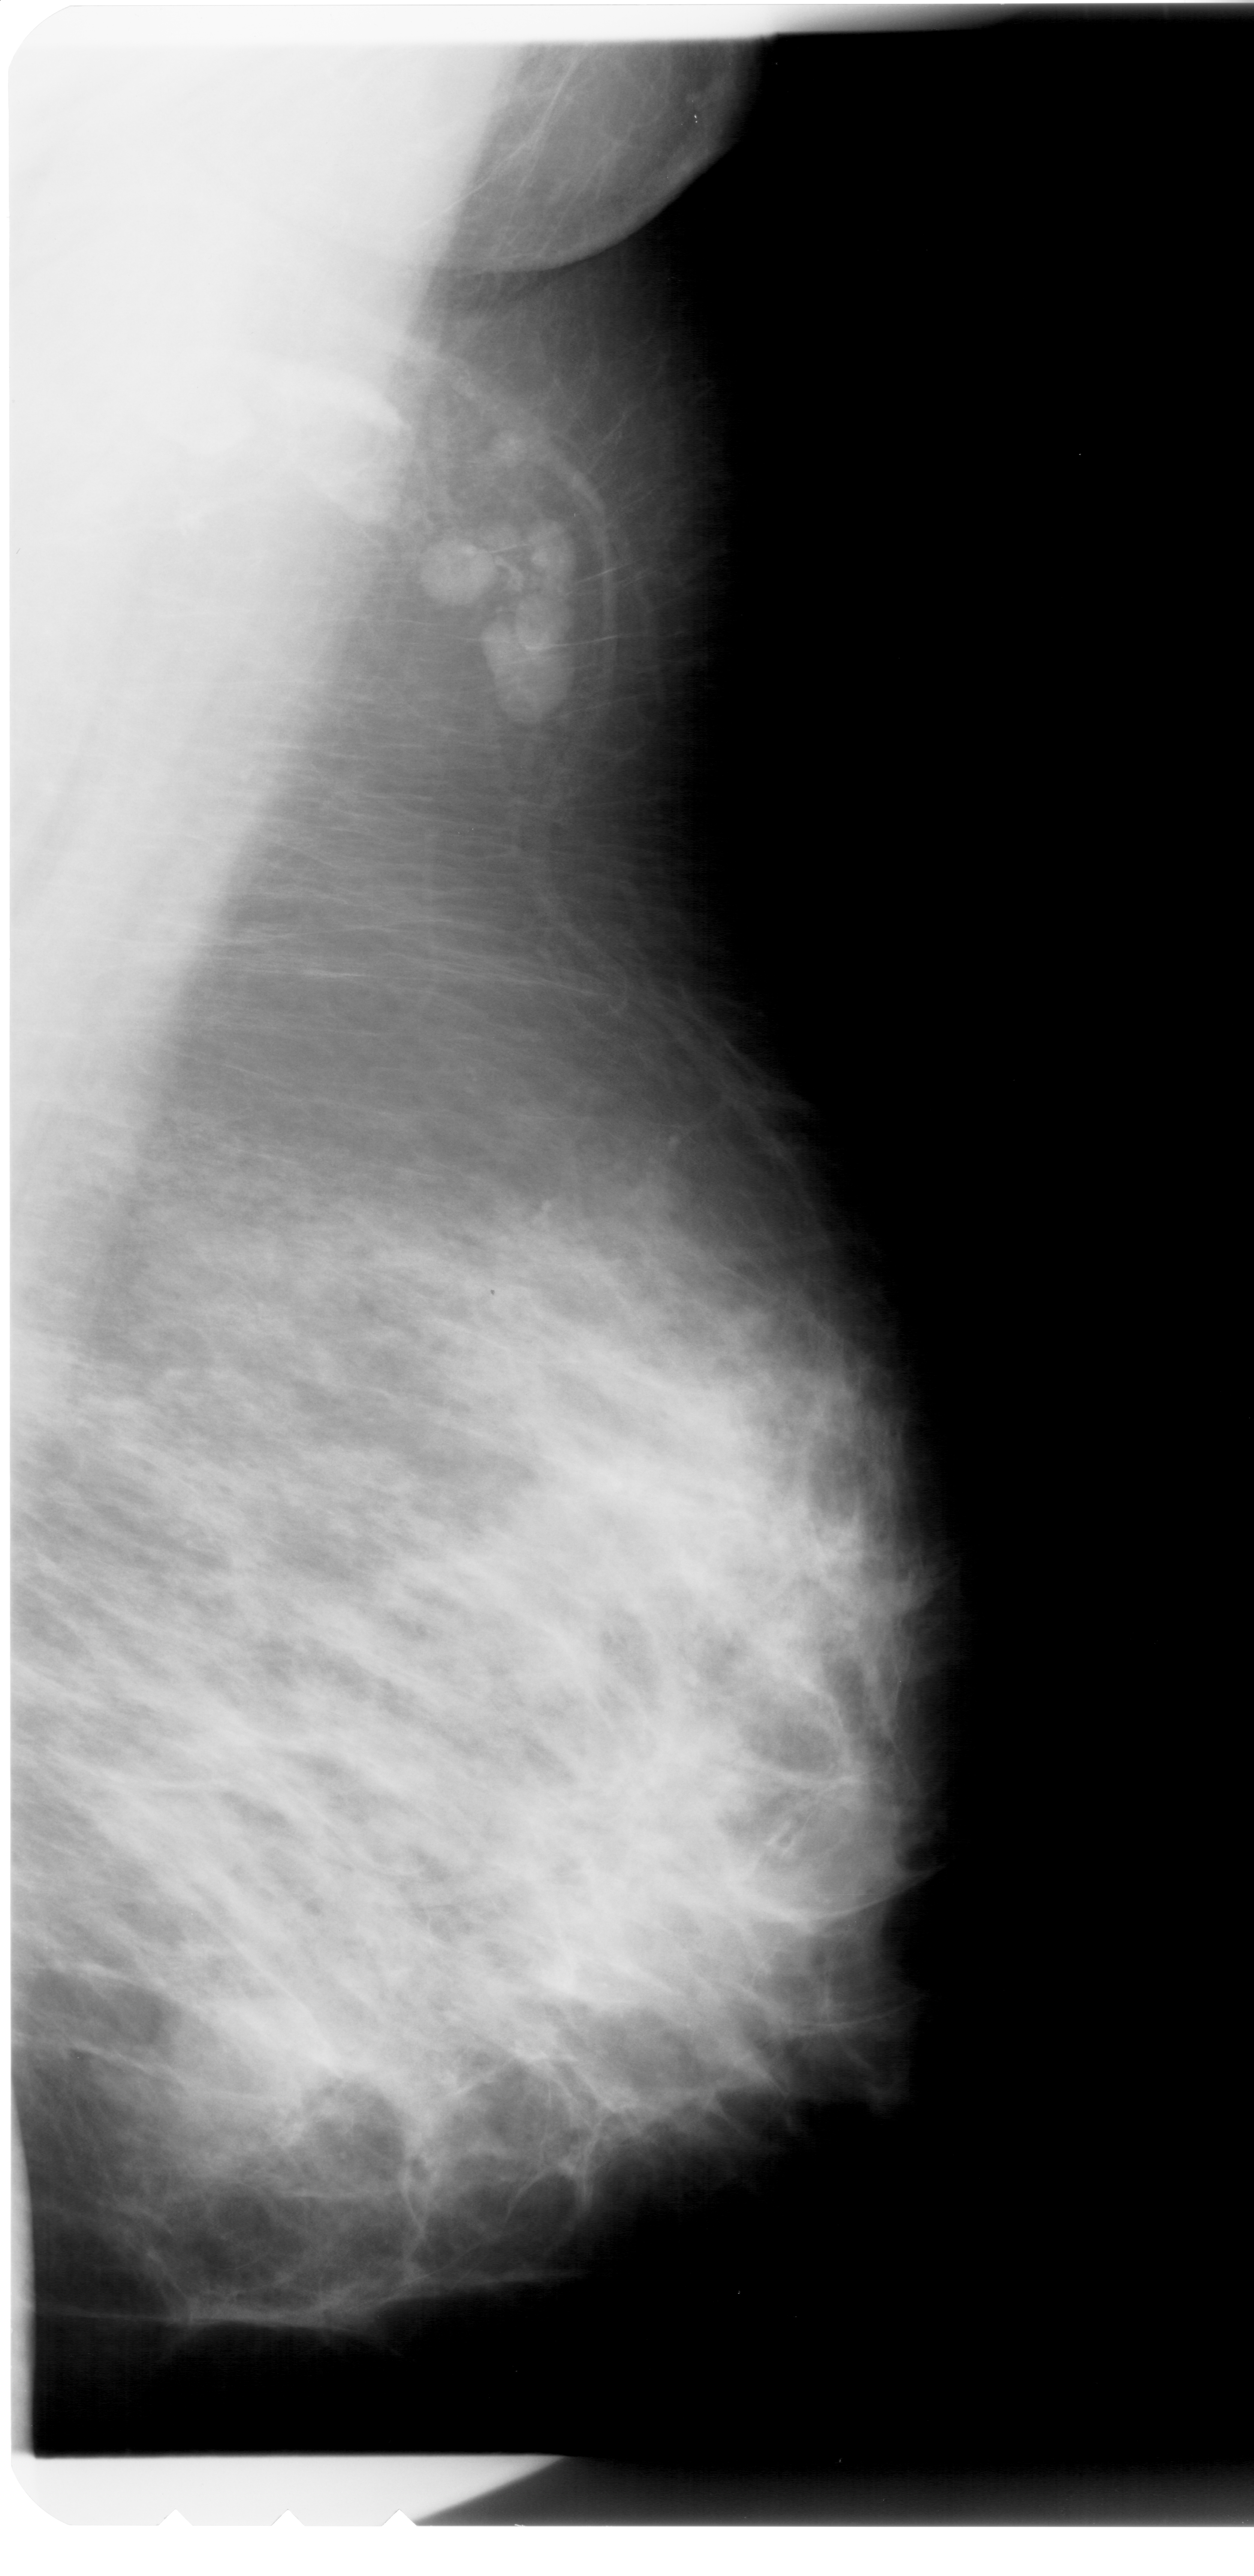
Digitized screen-film mammogram; right breast; MLO view.
Abnormality record for this image: mass, shape round, margins obscured; BI-RADS assessment category 4; subtlety rating 3 on a 1 (subtle) to 5 (obvious) scale; pathology (as recorded): benign.